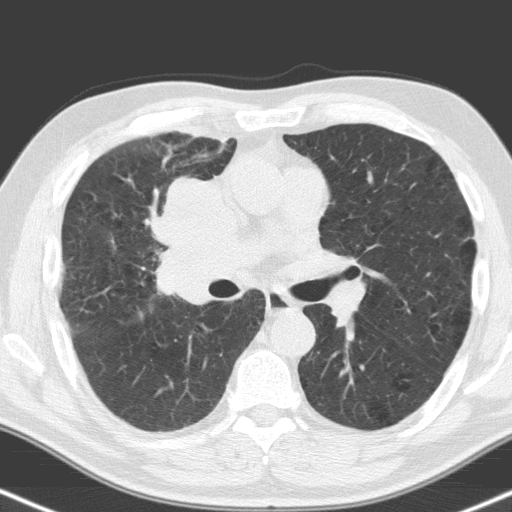
Low-dose screening chest CT, one axial slice. Slice 93 of 160 in the series (ordered by position). 120 kVp. Lung window (W 1500 / L -600 HU). 512 × 512 image matrix, field of view 324 × 324 mm.
Structures marked on this image (manually delineated by an expert):
- lesion 1 (tumor, hilum of right lung): bounding box [x1, y1, x2, y2] px = [157, 177, 244, 301]